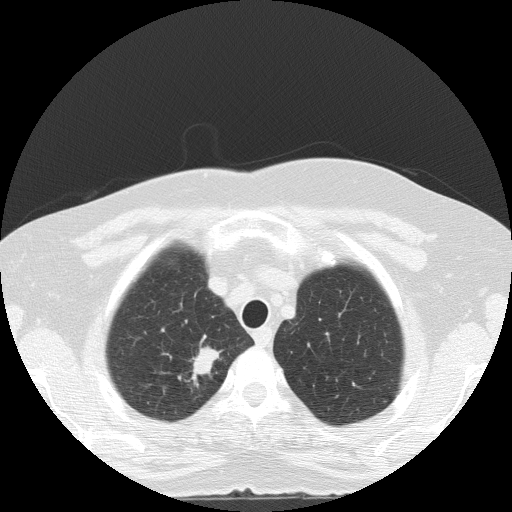
Low-dose screening chest CT, one axial slice. Position 114 of 133 along the scan axis. 120 kVp. Lung window (W 1500 / L -600 HU). 2 mm slice thickness. 512 × 512 image matrix, field of view 320 × 320 mm.
Annotated regions visible in this slice (expert manual segmentation):
- lesion 1 (tumor, upper lobe of right lung): box from (x=190, y=346) to (x=221, y=382) px